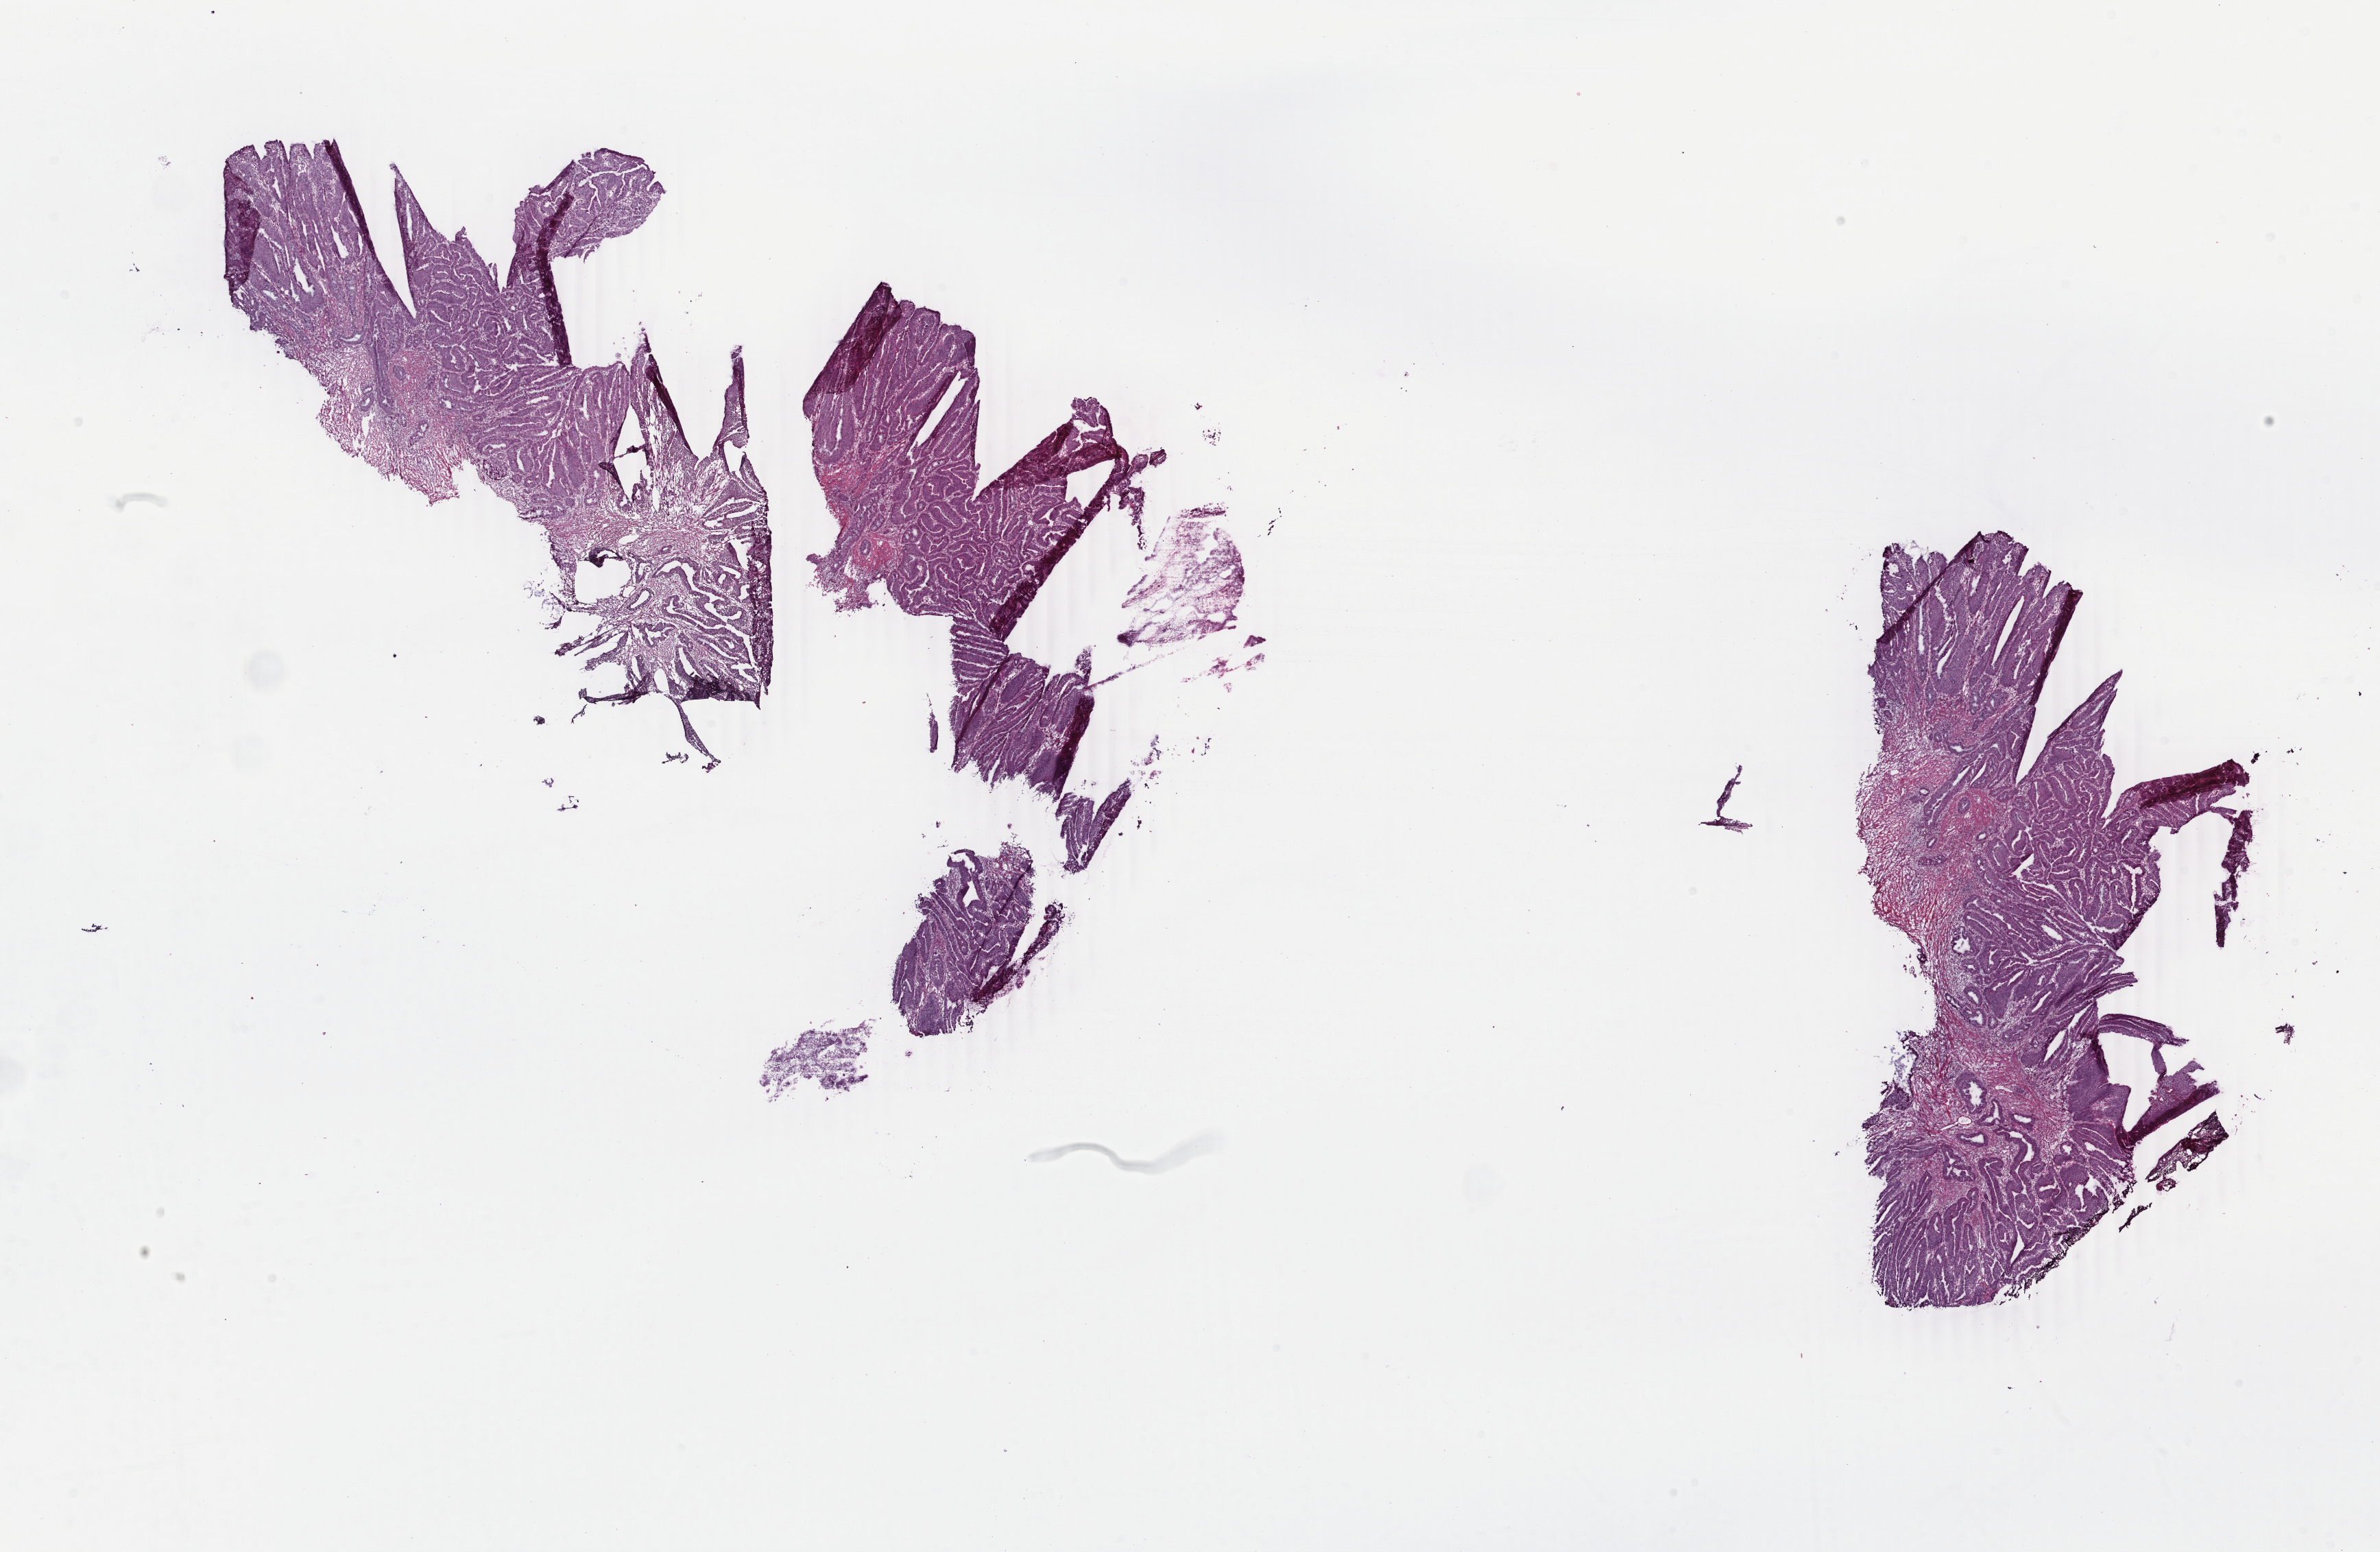
Digitized Hematoxylin and eosin (H&E) stained tissue section (whole slide) — a low-resolution overview of the entire scanned area, about 27.6 x 18.0 mm. Frozen section. Sample: primary tumour, rectum. Female, age 64 years at initial diagnosis. Slide review estimates, as recorded: tumour cells 90%, tumour nuclei 90%, normal cells 0%, stromal cells 9%, necrosis 1%. Inflammatory infiltration, as recorded: lymphocyte infiltration 5%, monocyte infiltration 2%, neutrophil infiltration 0%.
TNM: T1 N0 M0. AJCC pathologic stage: I (6th edition). Lymph nodes positive (case pathology): 0 of 18 examined. Pathologic diagnosis: Adenocarcinoma, NOS.